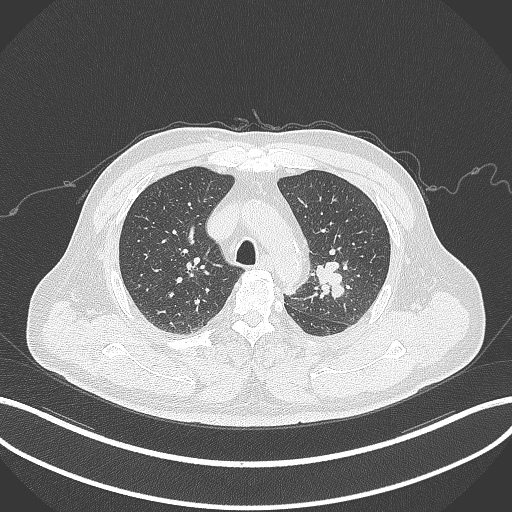
Chest CT, one axial slice. Slice 229 of 286 in the series (ordered by position). Reconstruction kernel B70f. 120 kVp. Lung window (W 1500 / L -600 HU). 1 mm slice thickness. 512 × 512 image matrix, field of view 400 × 400 mm. Patient: male, 67 years. From the clinical record (not read from this slice): clinical TNM (as recorded): T2a N1 M0; histopathological grade: G3.
Annotated regions visible in this slice (bounding box drawn by a radiologist):
- lung tumour (recorded histology: adenocarcinoma): bounding box <312,259,347,301> (left, top, right, bottom; pixels)